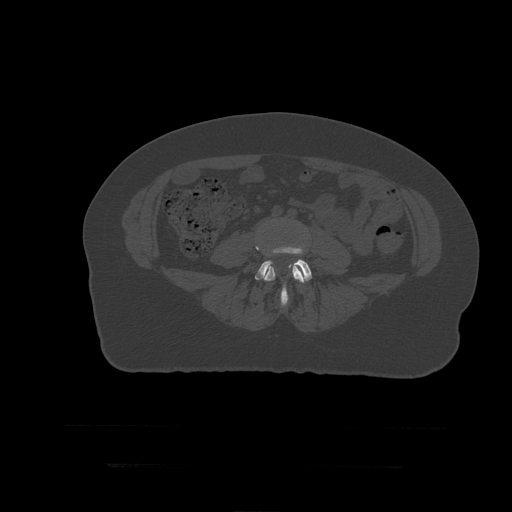
CT including the spine, one axial slice. Position 84 of 399 along the scan axis. Reconstruction kernel STANDARD. Bone window (W 1800 / L 400 HU). 1.25 mm slice thickness. 512 × 512 image matrix. Patient age 41 years. Case-level facts recorded for this patient, not image findings: primary cancer: breast.
Annotated regions visible in this slice (semi-automatically segmented with operator editing):
- L4 vertebra: bounding box <256,218,305,300> (left, top, right, bottom; pixels)
- L5 vertebra: <255,244,312,306>